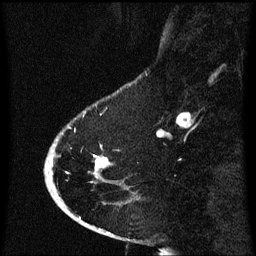
Breast MRI (dynamic contrast-enhanced), one sagittal slice; position 14 of 60 along the scan axis; dynamic contrast-enhanced series, image 2 of 3 at this slice position (ordered by acquisition); 1.5 T; TE 4.2 ms, TR 8.4 ms; 256 × 256 image matrix, field of view 200 × 200 mm. Female patient, age 53 years. From the clinical record (not read from this slice): setting: breast cancer imaged before/during neoadjuvant chemotherapy; receptor status: HR-positive, HER2-negative.
Outlined on this slice (semi-automatically segmented with operator editing):
- analysis volume of interest (the breast-tissue region the enhancement analysis was run in; not a lesion): bounding box <49,126,110,201> (left, top, right, bottom; pixels)
- tumour enhancement mask (voxels above the 70 % enhancement threshold inside the analysis volume of interest): <96,158,110,167>